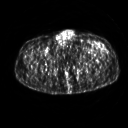
FDG PET of an extremity soft-tissue mass (from a PET/CT study), one axial slice; slice 261 of 267 in the series (ordered by position); 3.27 mm slice thickness; 128 × 128 image matrix. Patient: male, 64 years. Case-level facts recorded for this patient, not image findings: histological type: extraskeletal osteosarcoma; grade: high; site of the primary tumour: thigh.
Annotated regions visible in this slice (expert contour drawn on MRI and transferred to this co-registered scan by the dataset authors):
- gross tumour volume (mass): bounding box <94,43,105,49> (left, top, right, bottom; pixels)